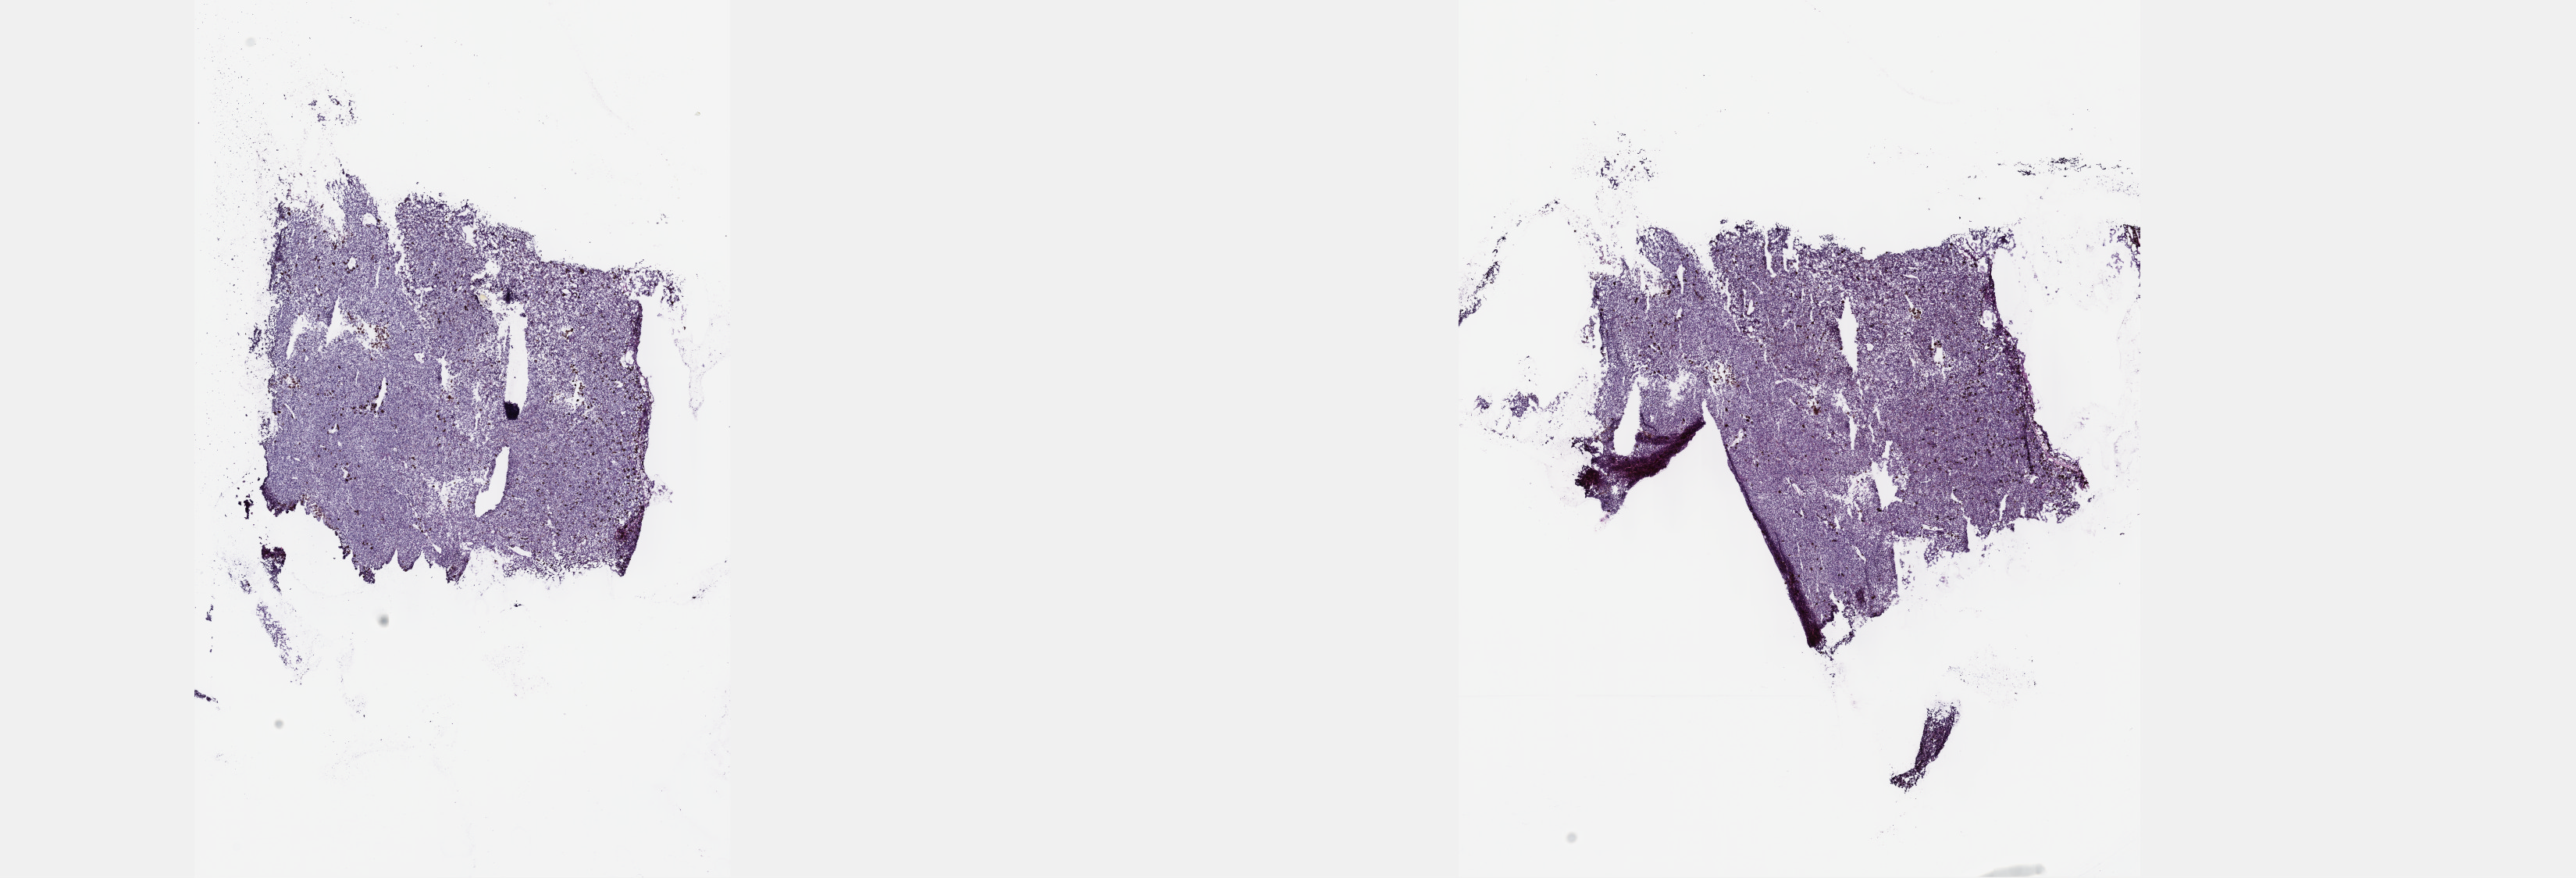
Whole-slide histology image, Hematoxylin and eosin (H&E) stained — low-resolution overview of the scanned area, about 26.7 x 9.1 mm (slide scanned at 40x). Frozen section. Sample: primary tumour, uvea. Female patient; age at initial diagnosis 51 years. Pathologist review of this section (percent, as recorded): tumour cells 100%, tumour nuclei 80%, normal cells 0%, stromal cells 0%, necrosis 0%. Inflammatory infiltration, as recorded: lymphocyte infiltration 2%, monocyte infiltration 0%, neutrophil infiltration 0%.
AJCC pathologic stage: IIIB. Diagnosis: Malignant melanoma, NOS (choroid).